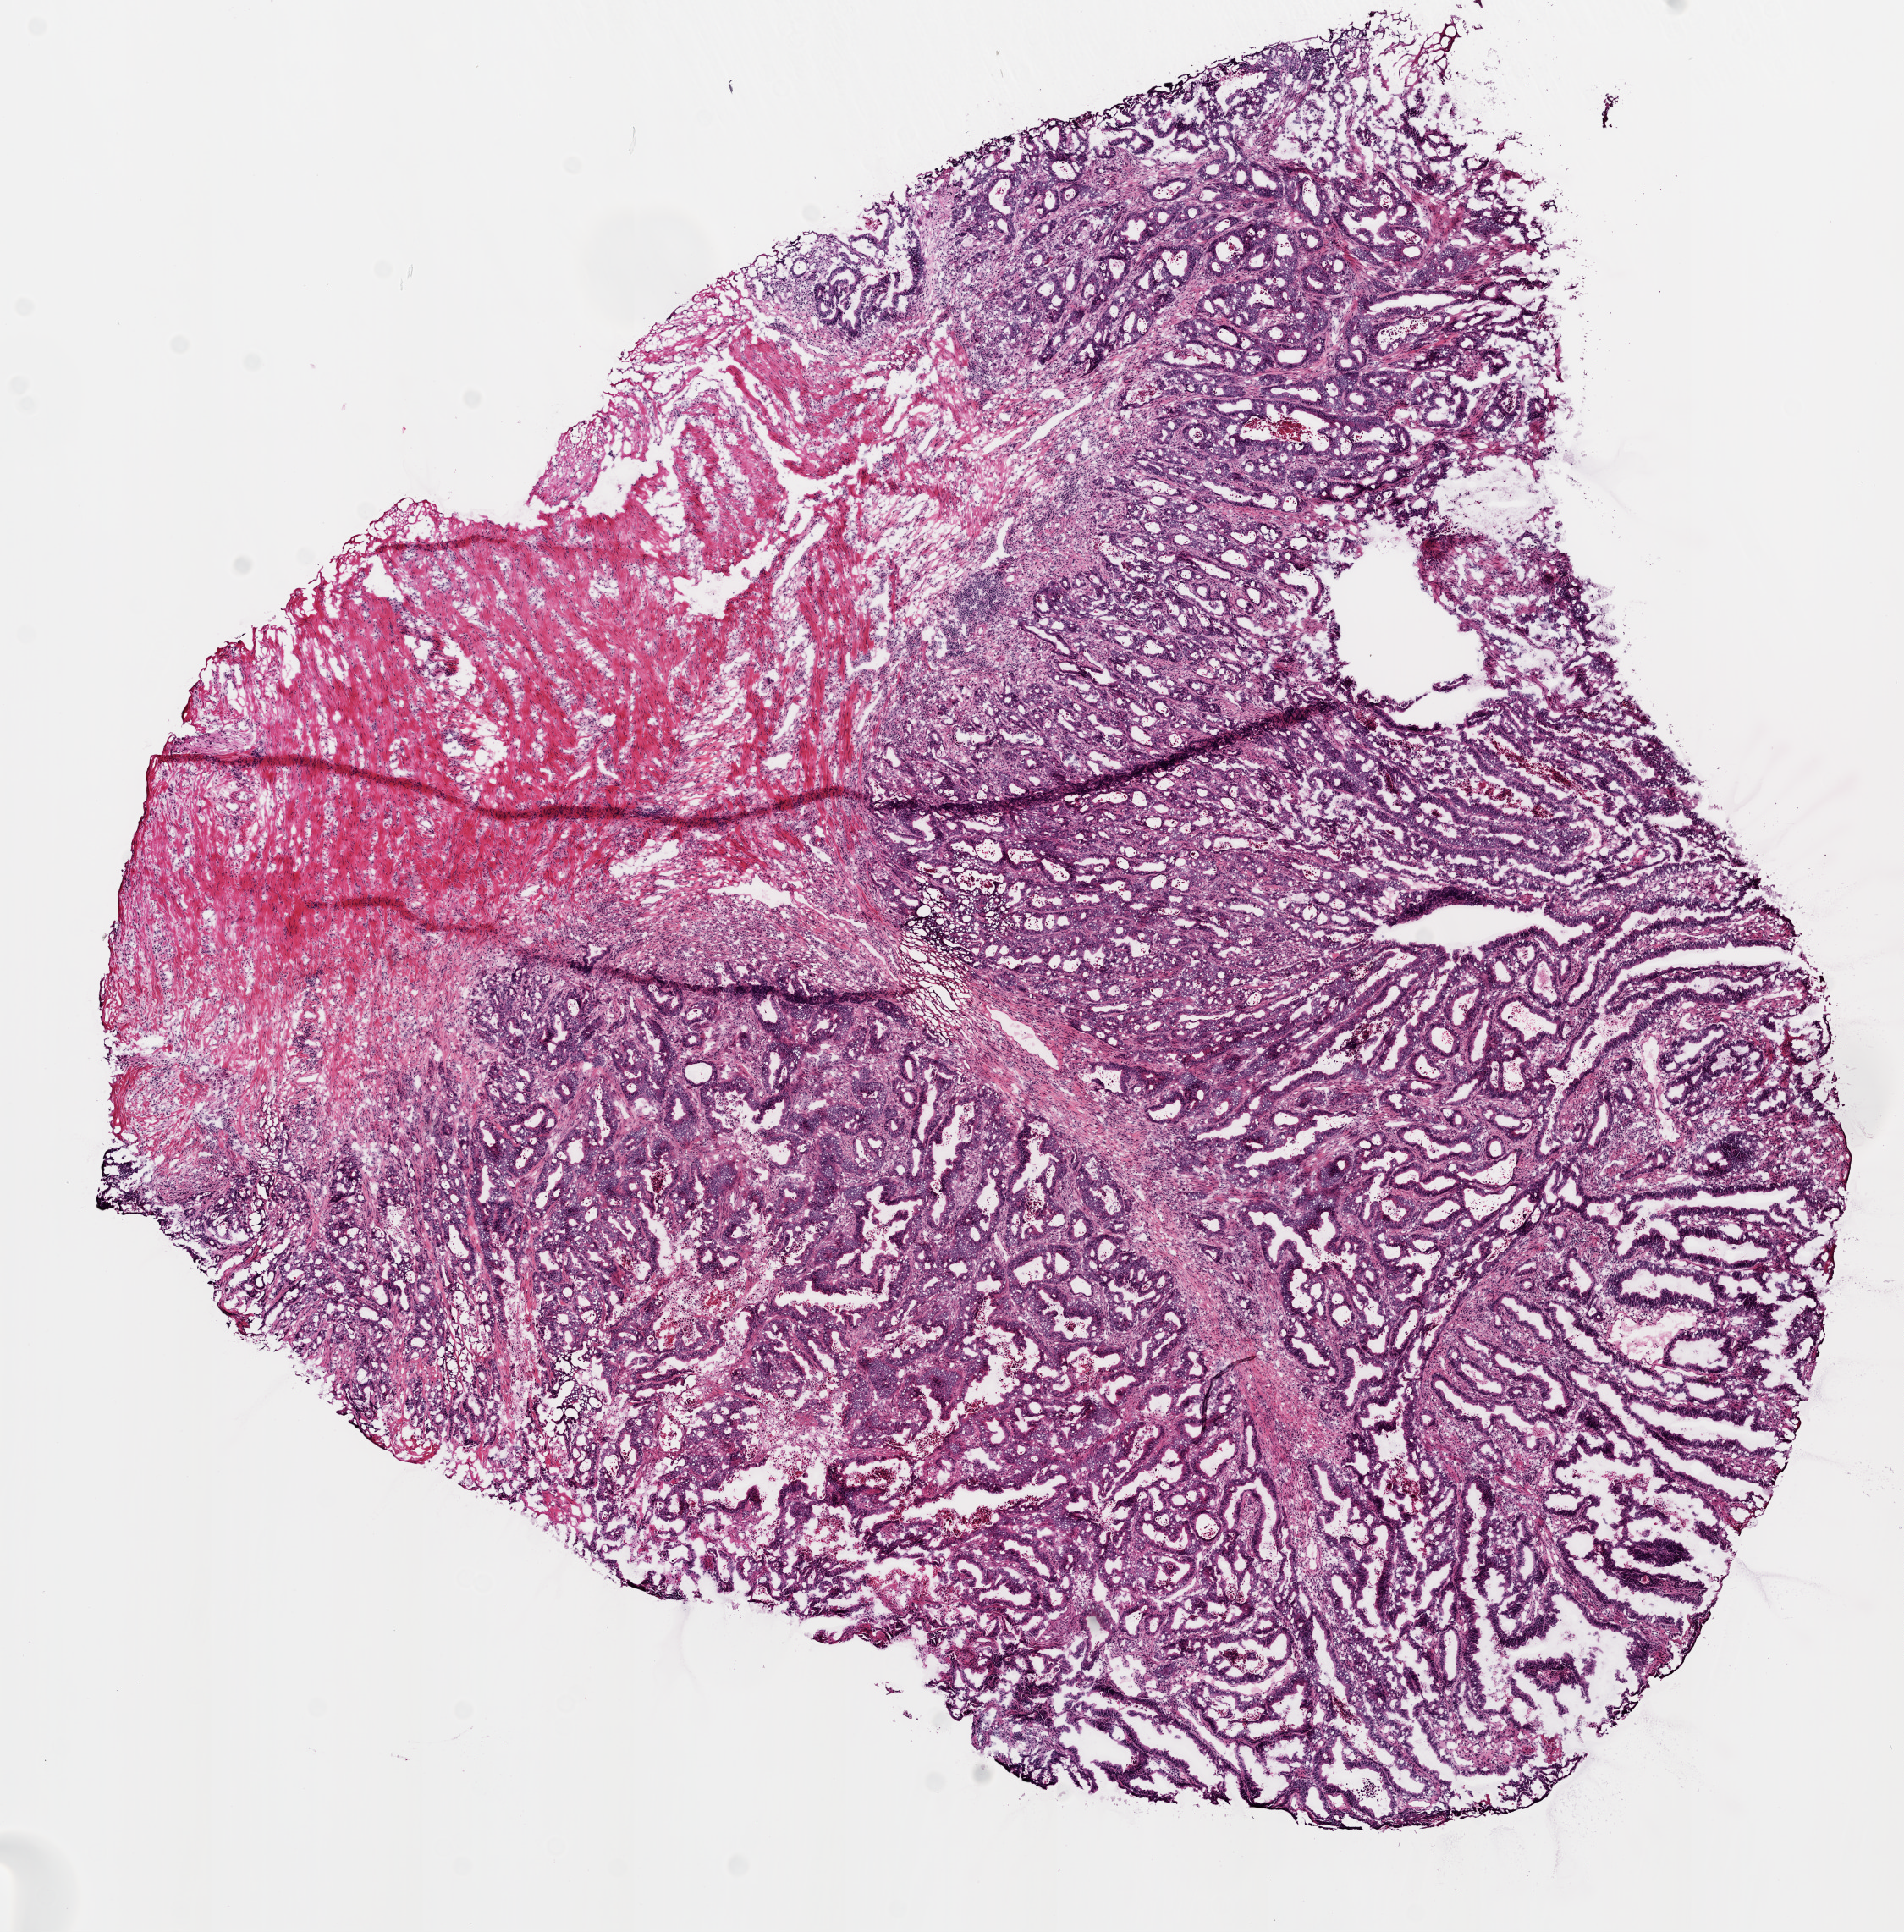
Digitized H&E tissue section (whole slide), shown as a low-resolution overview of the whole scanned area (about 9.0 x 9.2 mm), frozen section, rectum, primary tumour sample. Male patient; age at initial diagnosis 72 years. Slide review estimates, as recorded: tumour cells 80%, tumour nuclei 80%, normal cells 0%, stromal cells 15%, necrosis 5%.
• TNM: T3 N0 M0
• histologic diagnosis: Adenocarcinoma, NOS
• AJCC pathologic stage: IIA